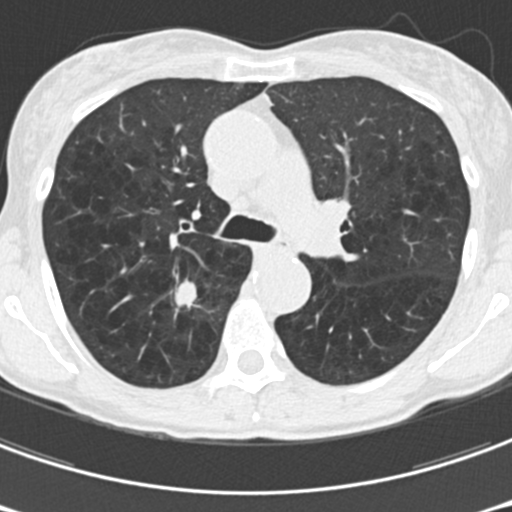
Low-dose screening chest CT, one axial slice; position 113 of 176 along the scan axis; reconstruction kernel B30f; lung window (W 1500 / L -600 HU); 512 × 512 image matrix, field of view 277 × 277 mm.
Structures marked on this image (outlined manually by an expert reader):
- lesion 1 (tumor, upper lobe of right lung): box from (x=175, y=277) to (x=196, y=308) px